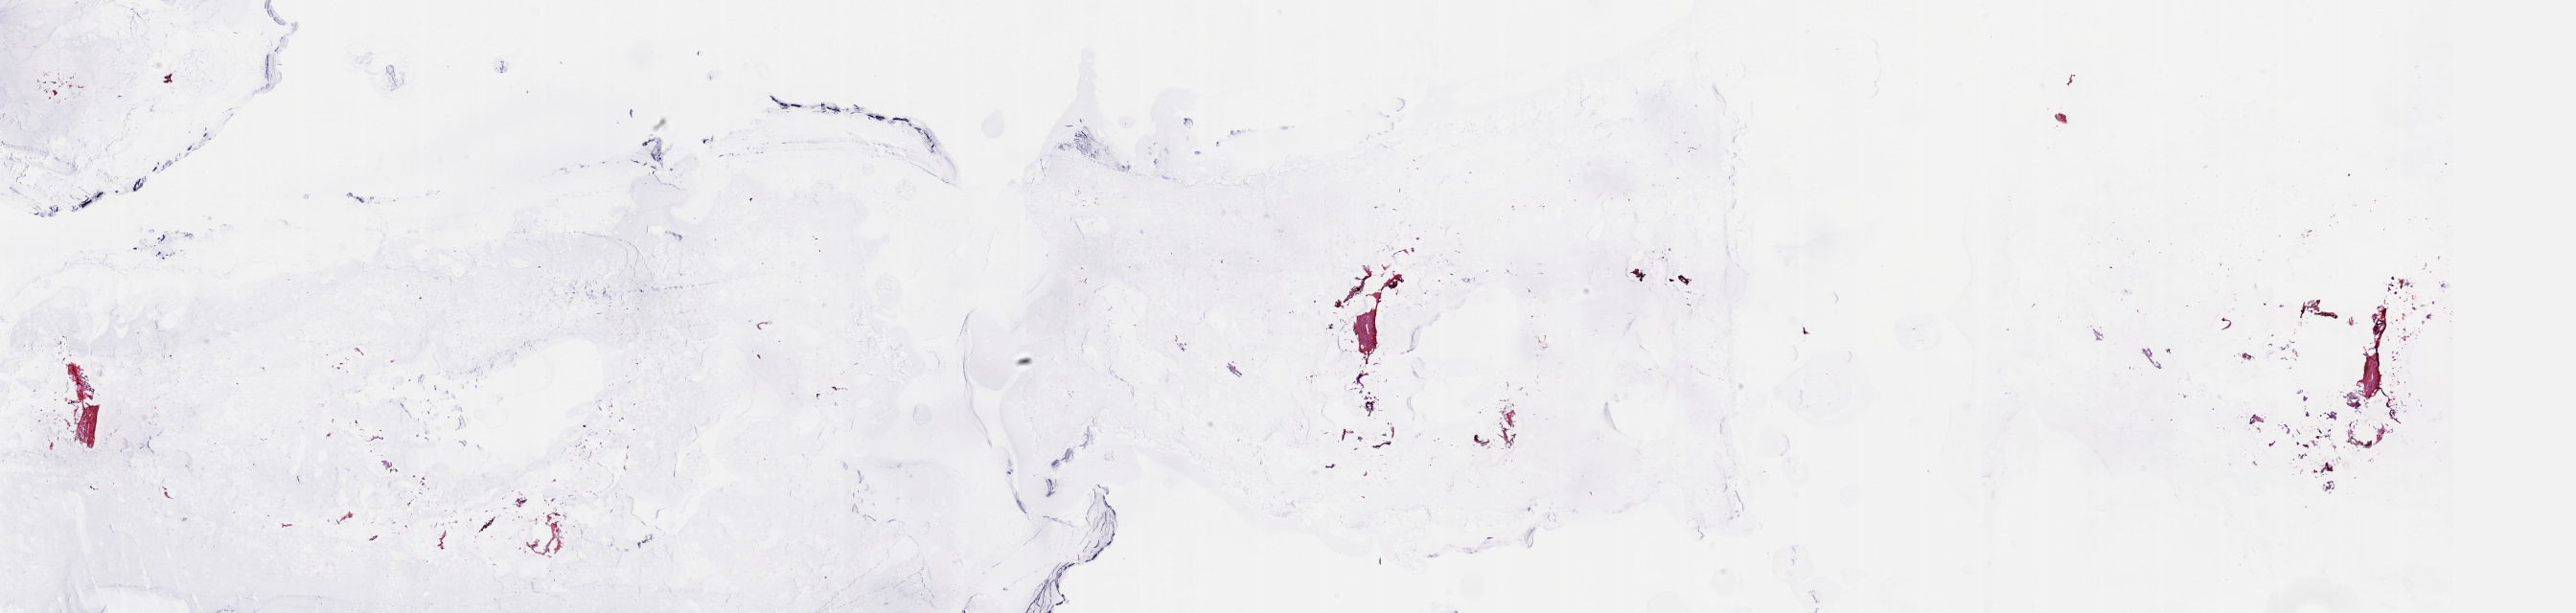
H&E whole-slide image — shown as a low-resolution overview of the whole scanned area (about 42.7 x 10.2 mm, slide scanned at 20x); frozen section from the top of the tissue portion; sample: solid tissue normal (non-tumour tissue), breast. Female patient; age at initial diagnosis 54 years. Composition of this section per pathologist review: tumour cells 0%, tumour nuclei 0%, normal cells 0%, stromal cells 100%, necrosis 0%. Inflammatory infiltration, as recorded: lymphocyte infiltration 0%, monocyte infiltration 0%, neutrophil infiltration 0%.
This section: solid tissue normal sample (biorepository sample class). Patient diagnosis: Infiltrating duct carcinoma, NOS.